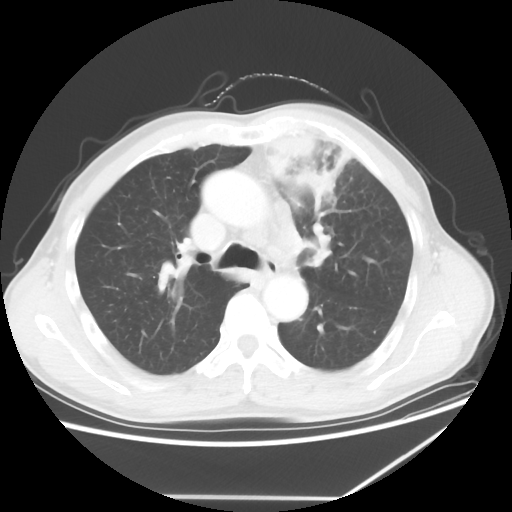
Chest CT, one axial slice. Reconstruction kernel STANDARD. 100 kVp. Lung window (W 1500 / L -600 HU). 512 × 512 image matrix, field of view 383 × 383 mm. Patient: male, 64 years. From the clinical record (not read from this slice): clinical TNM (as recorded): T1c N1 M1.
Outlined on this slice (bounding box drawn by a radiologist):
- lung tumour (recorded histology: squamous cell carcinoma): bounding box (x1, y1, x2, y2) in pixels: (252, 123, 353, 212)